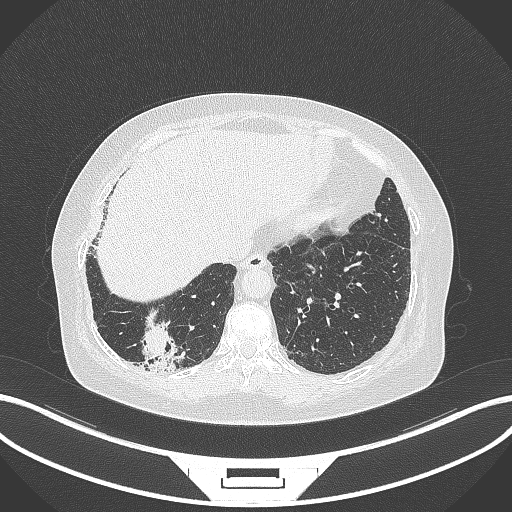
Chest CT, one axial slice; slice 34 of 296 in the series (ordered by position); reconstruction kernel B70f; lung window (W 1500 / L -600 HU); 1 mm slice thickness; 512 × 512 image matrix, field of view 400 × 400 mm. Patient: female, 65 years. Case-level facts recorded for this patient, not image findings: clinical TNM (as recorded): T2b N1 M0.
Annotated regions visible in this slice (bounding box drawn by a radiologist):
- lung tumour (recorded histology: adenocarcinoma): box from (x=135, y=309) to (x=184, y=374) px